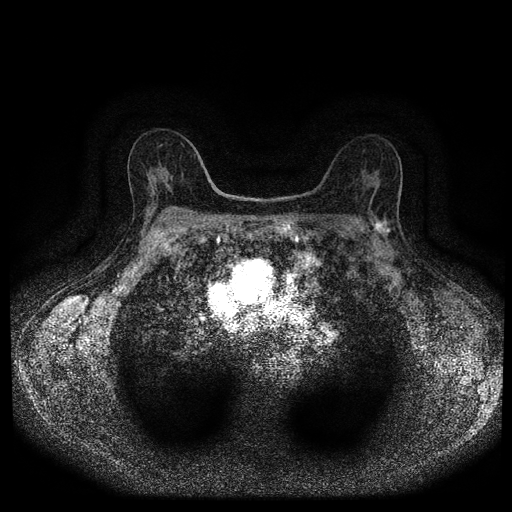
Breast MRI (dynamic contrast-enhanced, multi-phase), one axial slice. Slice 59 of 116 in the series (ordered by position). Dynamic contrast-enhanced series, time point 2 of 5 at this slice position (early post-contrast). 1.5 T. TE 2.7 ms, TR 5.4 ms. 512 × 512 image matrix, field of view 330 × 330 mm. Patient: female, 63 years.
Annotated regions visible in this slice (semi-automatic segmentation, software-assisted and operator-edited):
- breast lesion (labelled 'tumour' in the annotation; benign lesions carry a separate 'benign' label): box from (x=372, y=217) to (x=397, y=241) px